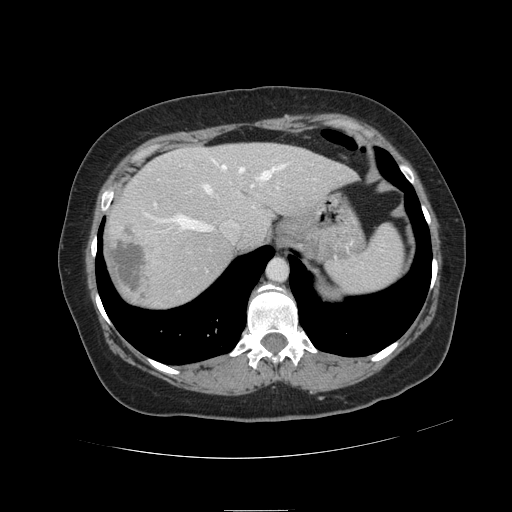
Contrast-enhanced abdominal CT, one axial slice. Slice 94 of 121 in the series (ordered by position). 120 kVp. Intravenous contrast given. Soft-tissue window (W 400 / L 40 HU). 2.5 mm slice thickness. 512 × 512 image matrix. Female patient, age 52 years. Case-level facts recorded for this patient, not image findings: diagnosis: colorectal cancer liver metastases, imaged before liver resection; multiple liver metastases: yes; largest metastasis: 6.3 cm; disease in both lobes: no.
Annotated regions visible in this slice (expert manual segmentation):
- hepatic veins: box from (x=144, y=159) to (x=284, y=232) px
- liver: (x=105, y=144)–(x=354, y=310)
- planned liver remnant (the part of the liver to remain after resection): (x=169, y=144)–(x=354, y=244)
- portal vein (with intrahepatic branches): (x=154, y=187)–(x=279, y=206)
- liver metastasis: (x=109, y=223)–(x=147, y=299)